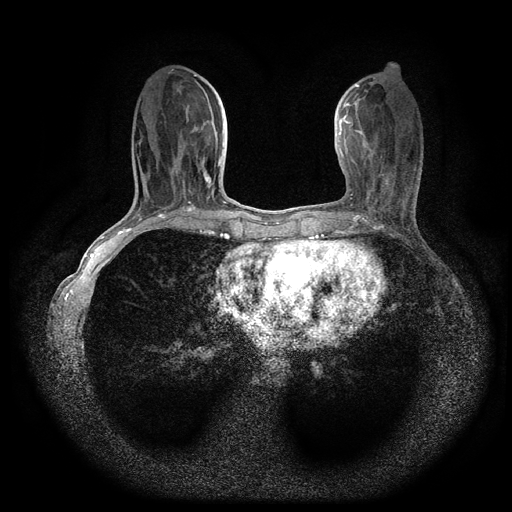
Breast MRI (dynamic contrast-enhanced, multi-phase), one axial slice; slice 36 of 116 in the series (ordered by position); dynamic contrast-enhanced series, time point 2 of 5 at this slice position (early post-contrast); 1.5 T; TE 2.7 ms, TR 5.4 ms; 2 mm slice thickness; 512 × 512 image matrix. Patient: female, 49 years.
Structures marked on this image (semi-automatic segmentation, software-assisted and operator-edited):
- breast lesion (labelled benign in the annotation): bounding box <202,168,215,188> (left, top, right, bottom; pixels)